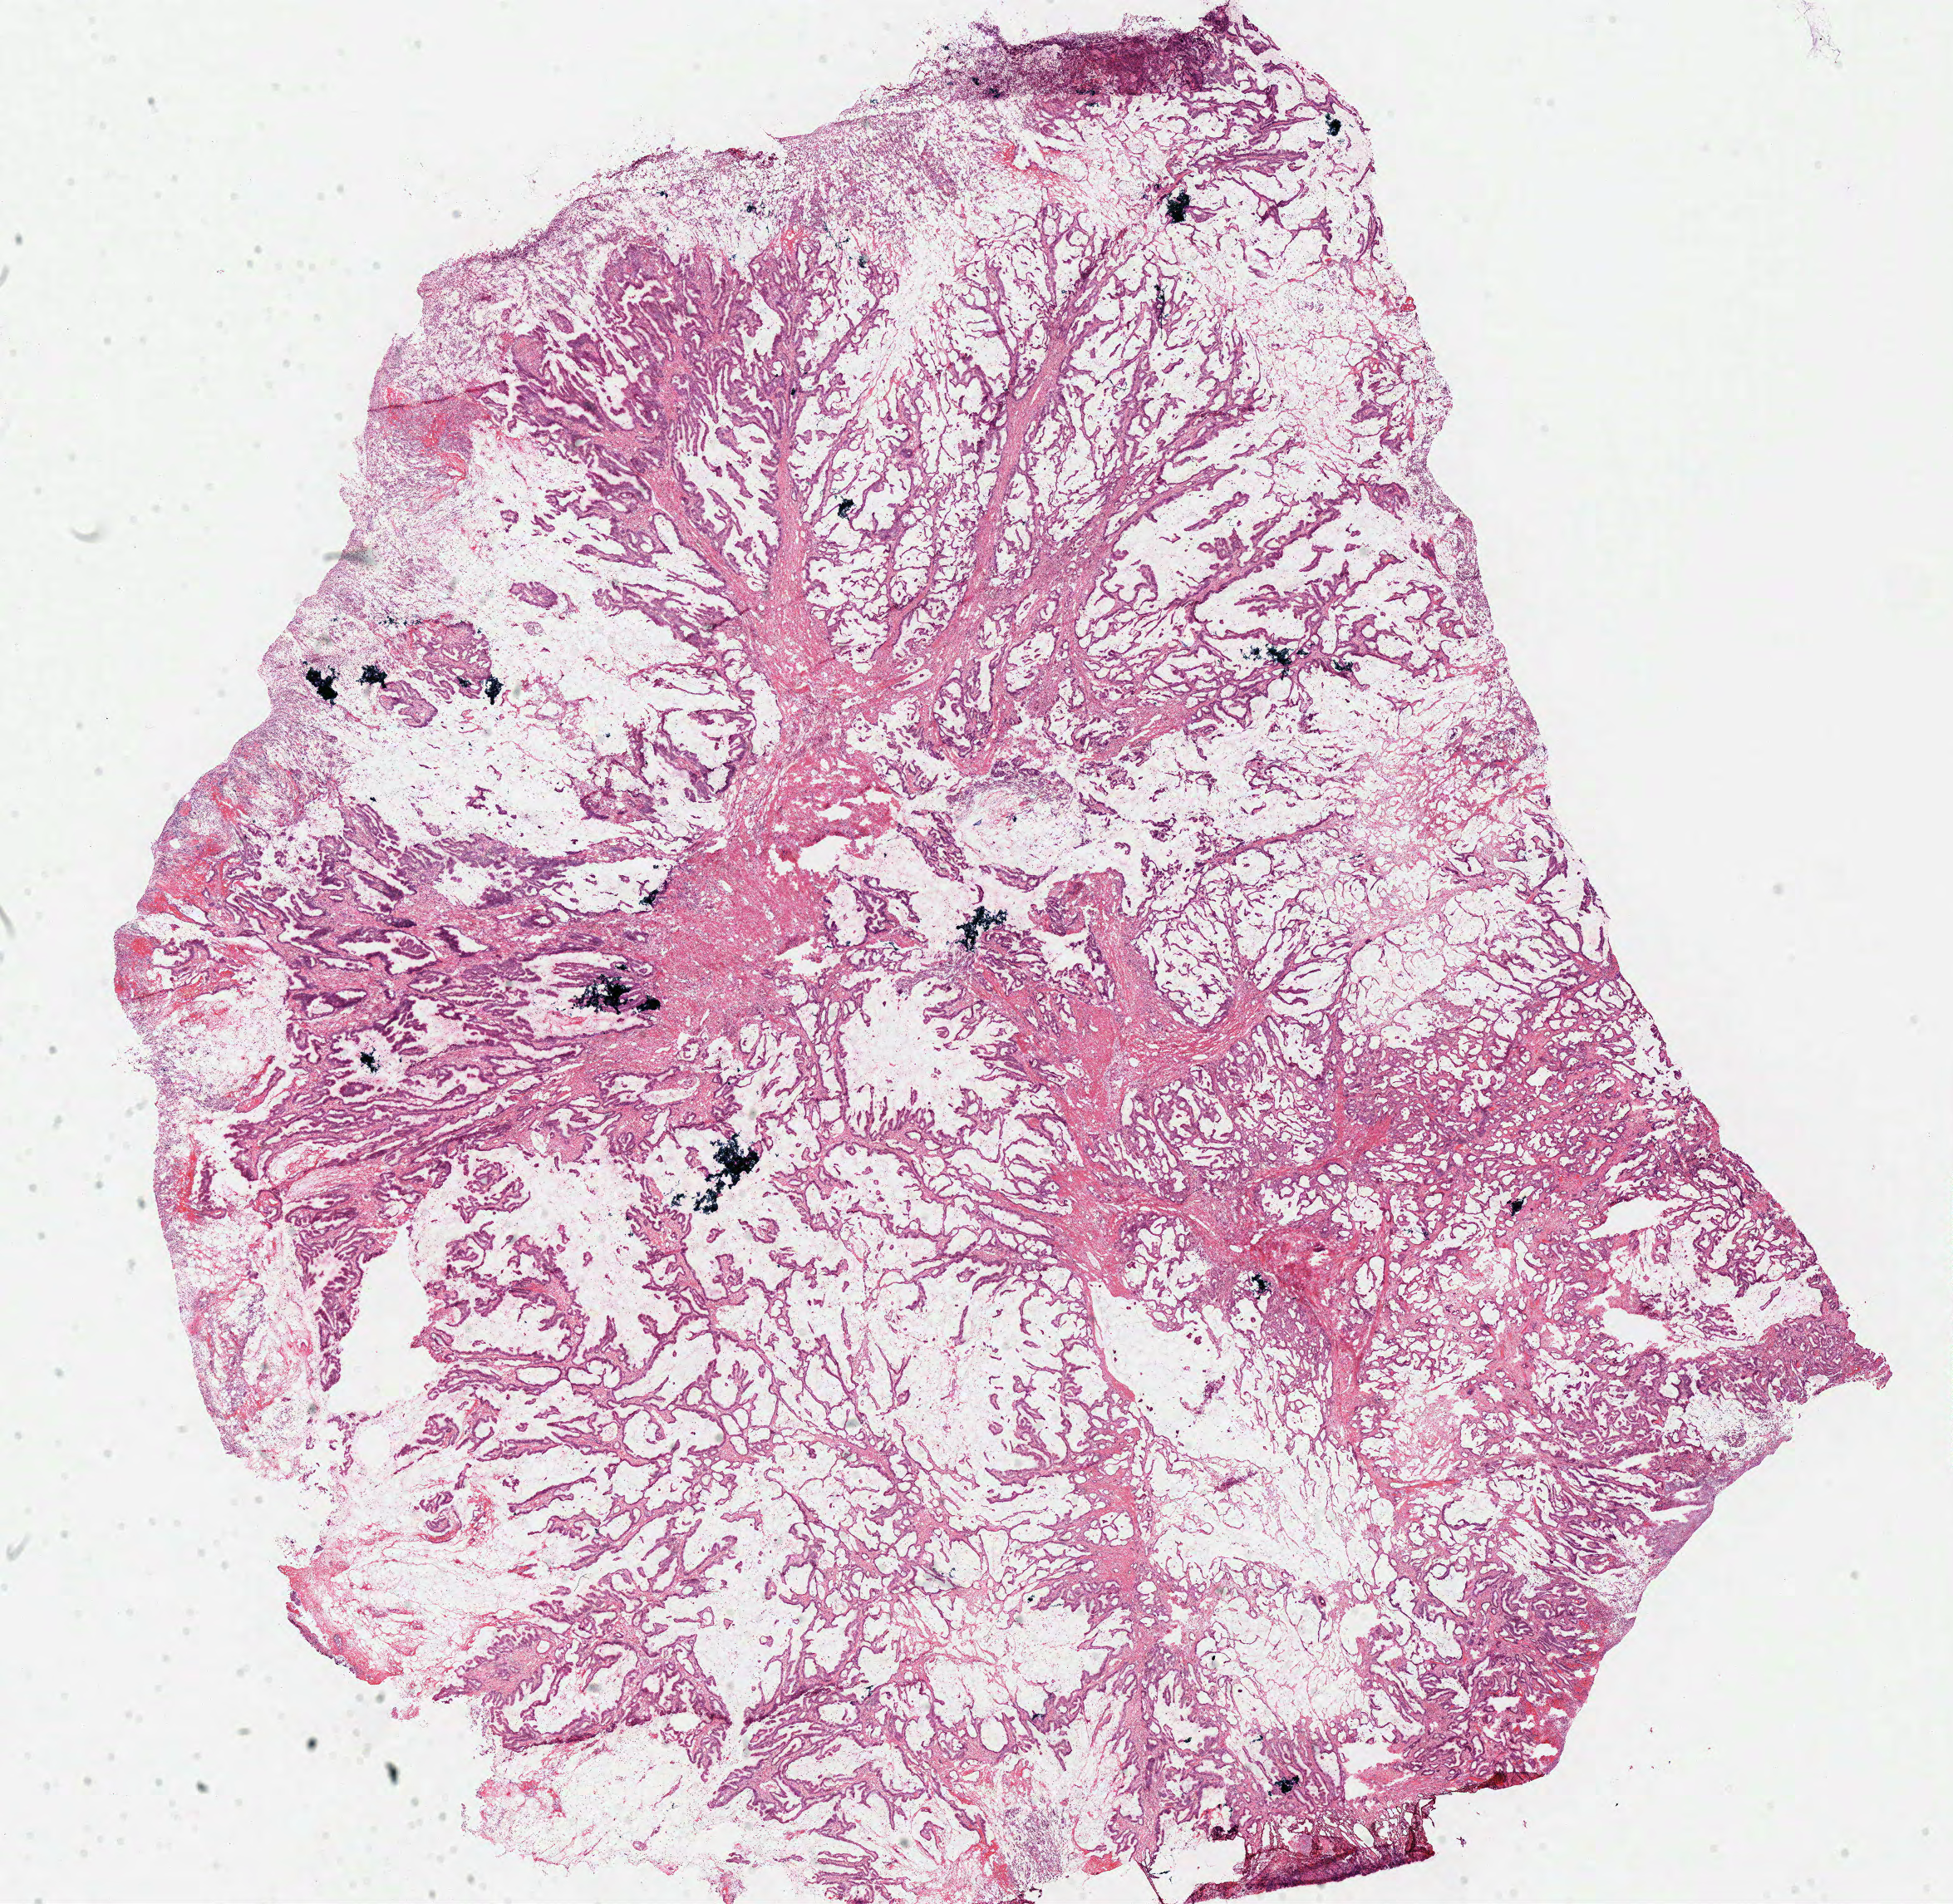
H&E whole-slide image, low-resolution overview of the scanned area, about 18.5 x 18.1 mm (from a 40x scan), frozen section, primary tumour sample from the colon. Patient: female, age at initial diagnosis 63 years. Pathologist review of this section (percent, as recorded): tumour cells 100%, tumour nuclei 80%, normal cells 0%, stromal cells 0%, necrosis 0%. Infiltration values recorded for this section: lymphocyte infiltration 5%, monocyte infiltration 1%, neutrophil infiltration 1%.
* lymph nodes positive (case pathology): 0 of 28 examined
* diagnosis: Adenocarcinoma, NOS (cecum)
* AJCC pathologic stage: IIA (7th edition)